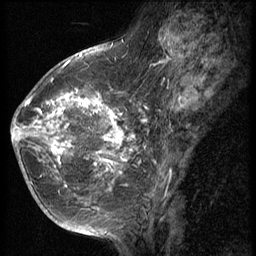
Breast MRI (dynamic contrast-enhanced), one sagittal slice. Slice 24 of 56 in the series (ordered by position). 3 images stored at this slice position (order not interpretable as contrast timing). 1.5 T. TE 4.2 ms, TR 9 ms. 2.5 mm slice thickness. 256 × 256 image matrix. Patient: female, 49 years. Case-level facts recorded for this patient, not image findings: setting: breast cancer imaged before/during neoadjuvant chemotherapy; receptor status: HER2-positive.
Structures marked on this image (semi-automatically segmented with operator editing):
- analysis volume of interest (the breast-tissue region the enhancement analysis was run in; not a lesion): bounding box <13,79,134,203> (left, top, right, bottom; pixels)
- tumour enhancement mask (voxels above the 140 % enhancement threshold inside the analysis volume of interest): <13,90,133,176>